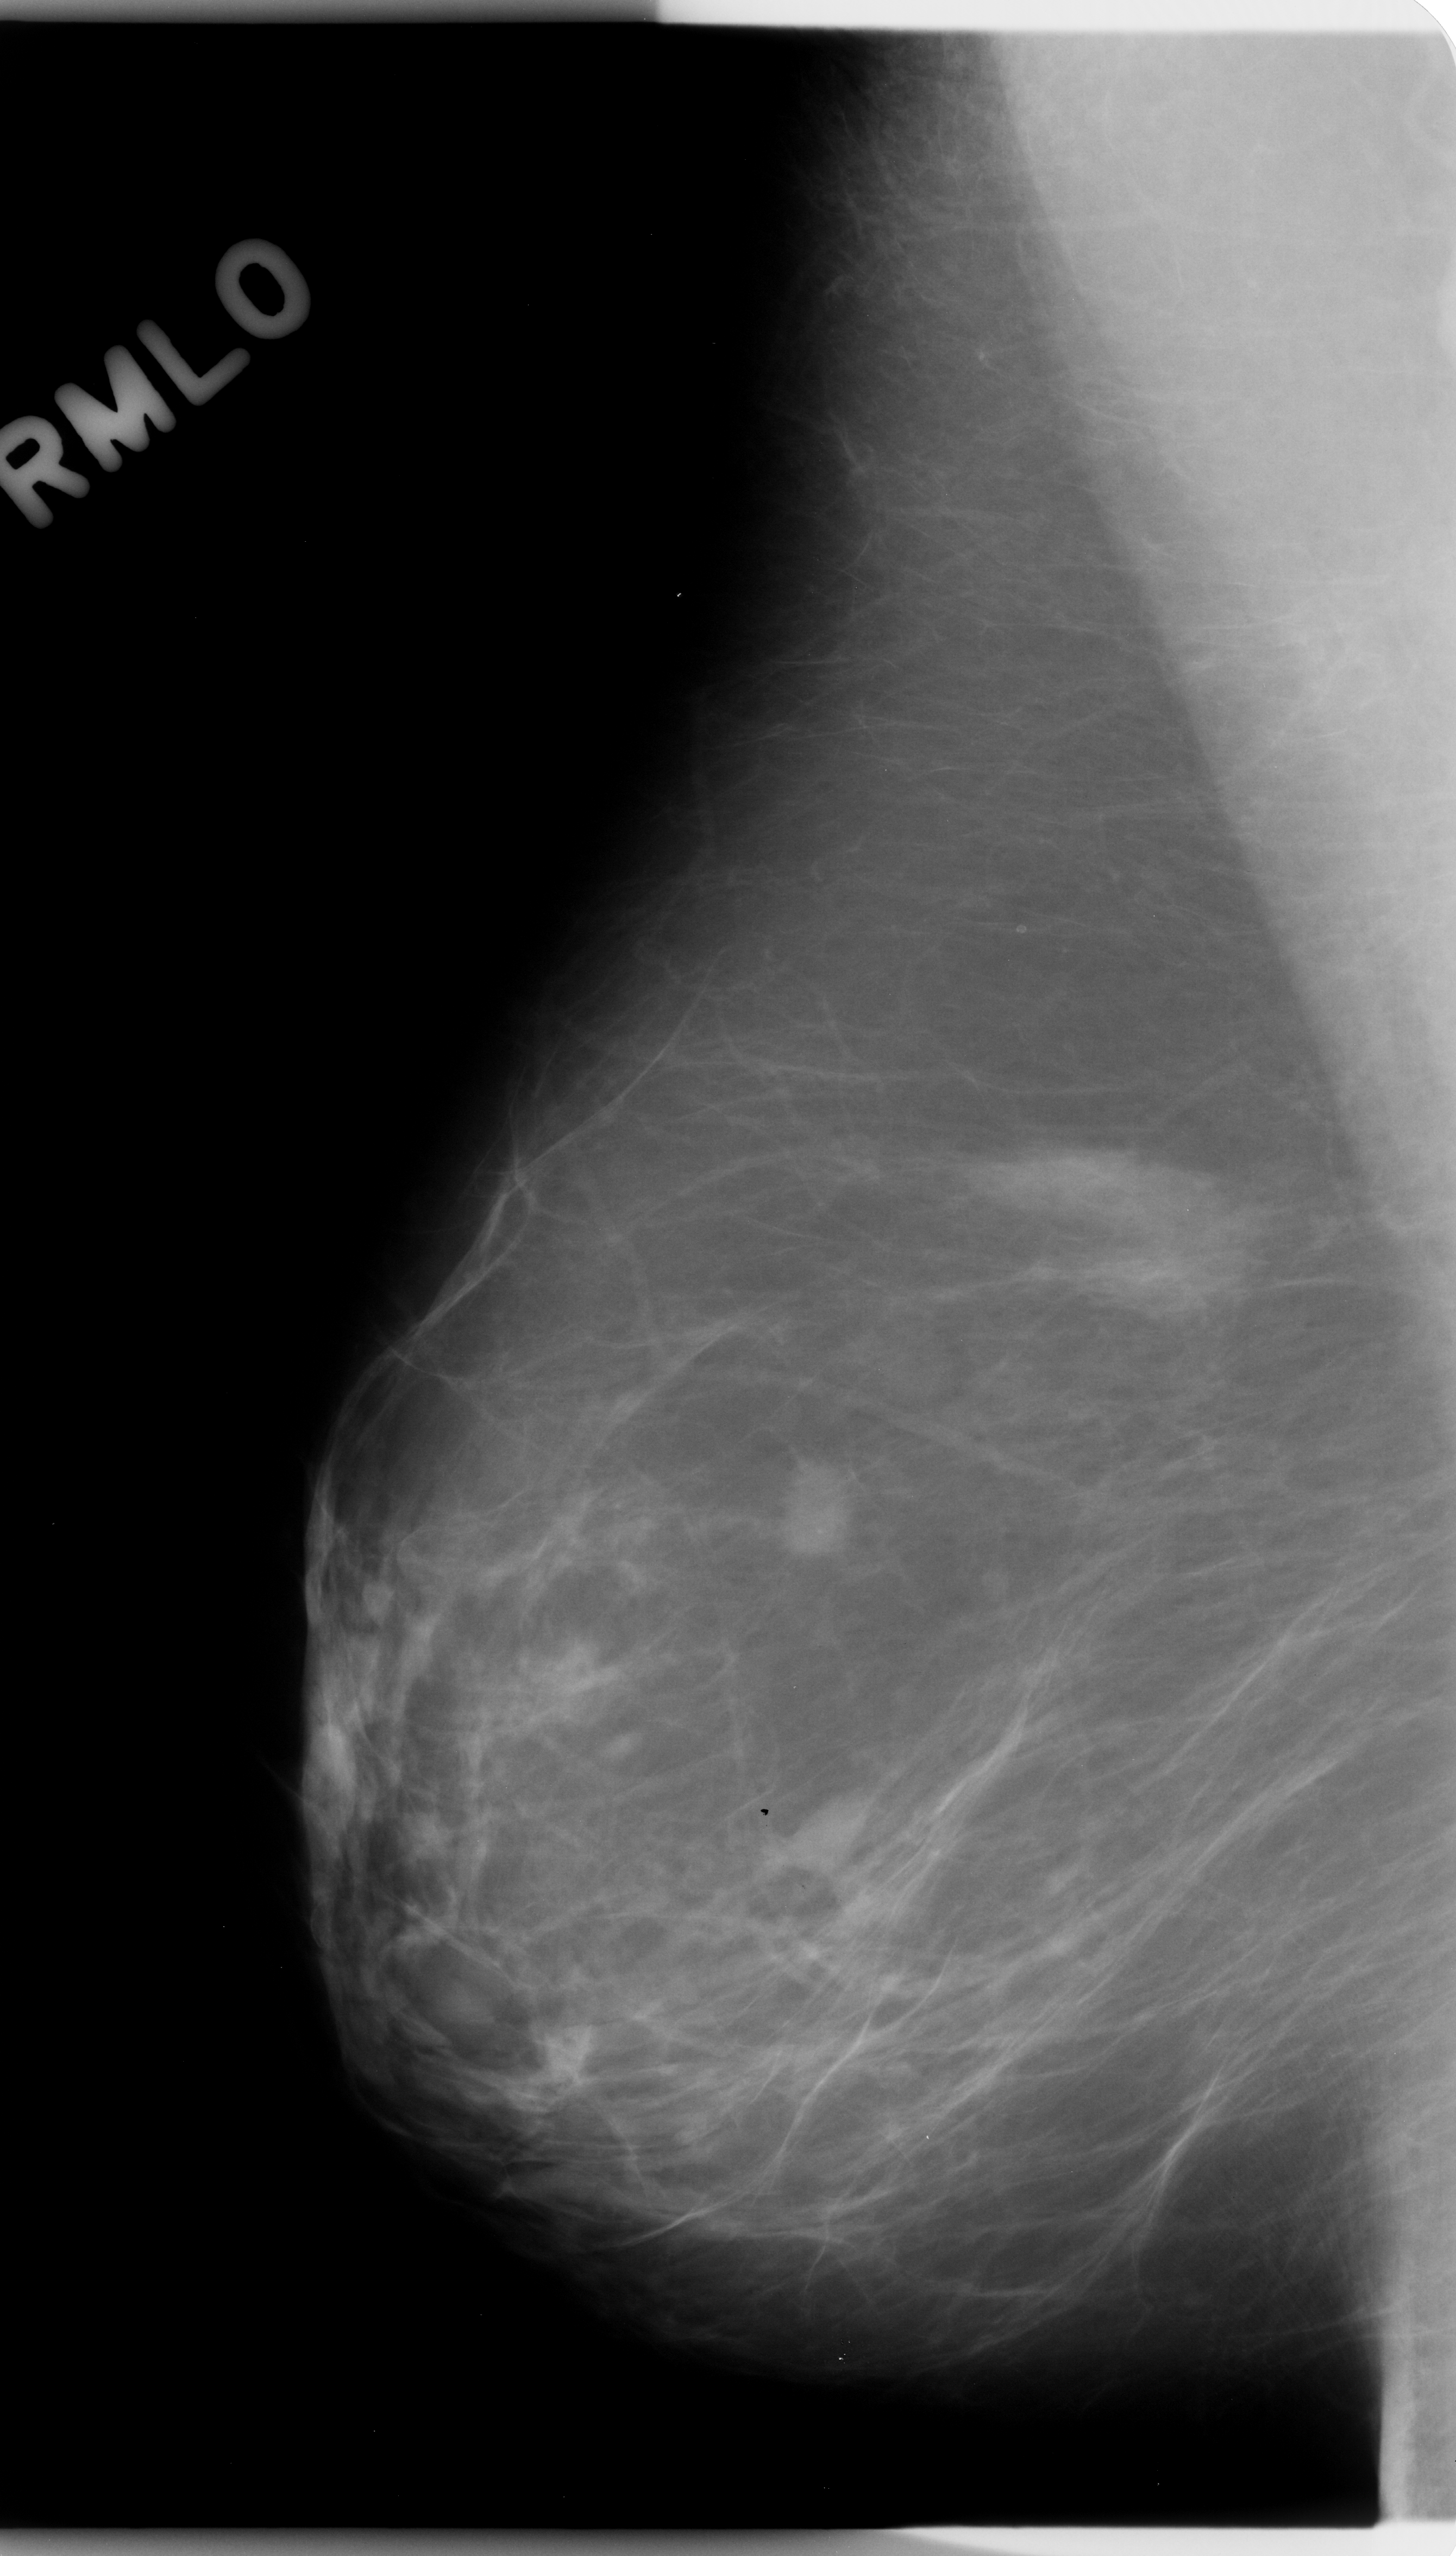
Digitized screen-film mammogram. Right breast. Mediolateral oblique (MLO) view. BI-RADS breast density category 1 (scale 1–4). 1456 × 2556 image matrix.
Expert-marked regions of interest on this film, with their recorded descriptors:
- mass, shape oval, margins spiculated; BI-RADS assessment category 5; pathology result (as recorded, not read from the image): malignant: bounding box [x1, y1, x2, y2] px = [710, 1444, 868, 1569]